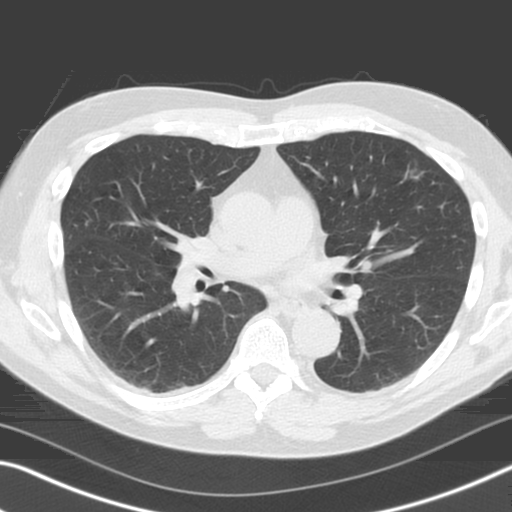
Low-dose screening chest CT, one axial slice; 120 kVp; lung window (W 1500 / L -600 HU); 3.2 mm slice thickness; 512 × 512 image matrix, field of view 340 × 340 mm.
Structures marked on this image (expert manual segmentation):
- lesion 1 (tumor, upper lobe of left lung): bounding box [x1, y1, x2, y2] px = [409, 165, 426, 179]